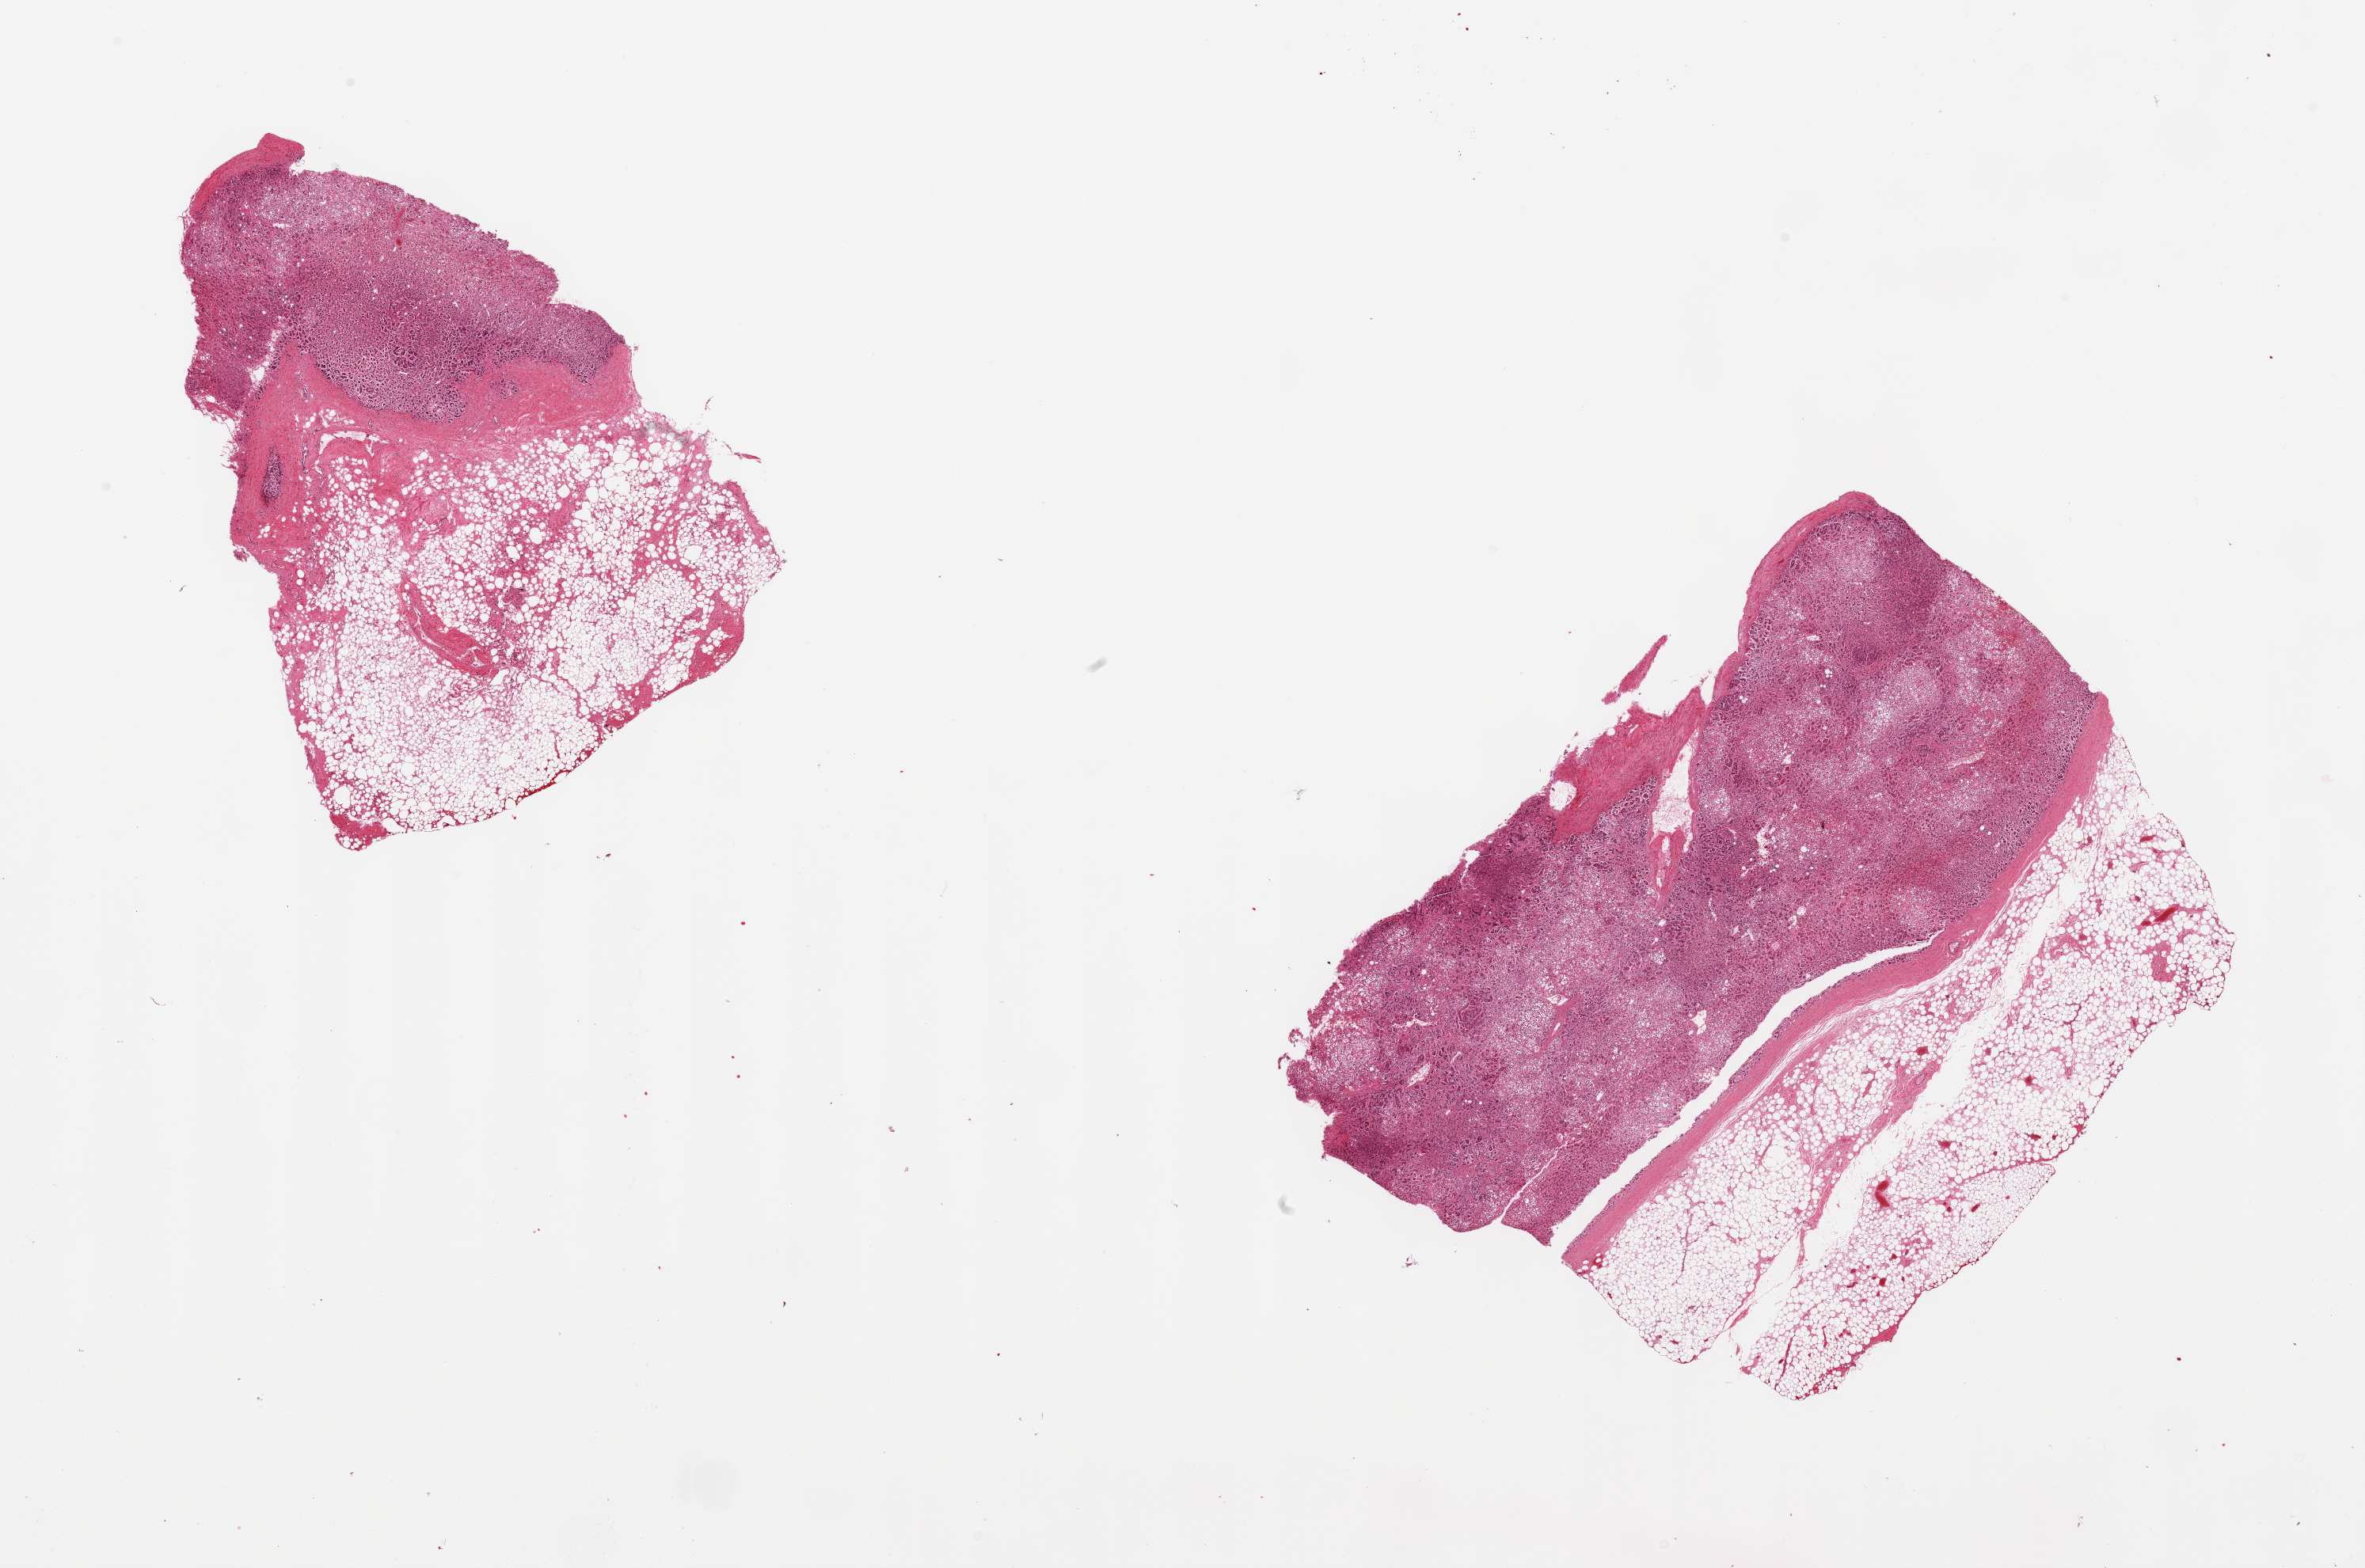
Digitized H&E-stained section — whole scanned area (about 23.6 x 15.7 mm, slide scanned at 20x) shown as a low-resolution overview; PAXgene-fixed paraffin-embedded (PFPE) section; sampled site (target tissue): adrenal gland; tissue donor sample. Donor: male.
- review note (as recorded): 2 pieces; up to 4mm external fat content along 1 side of each piece